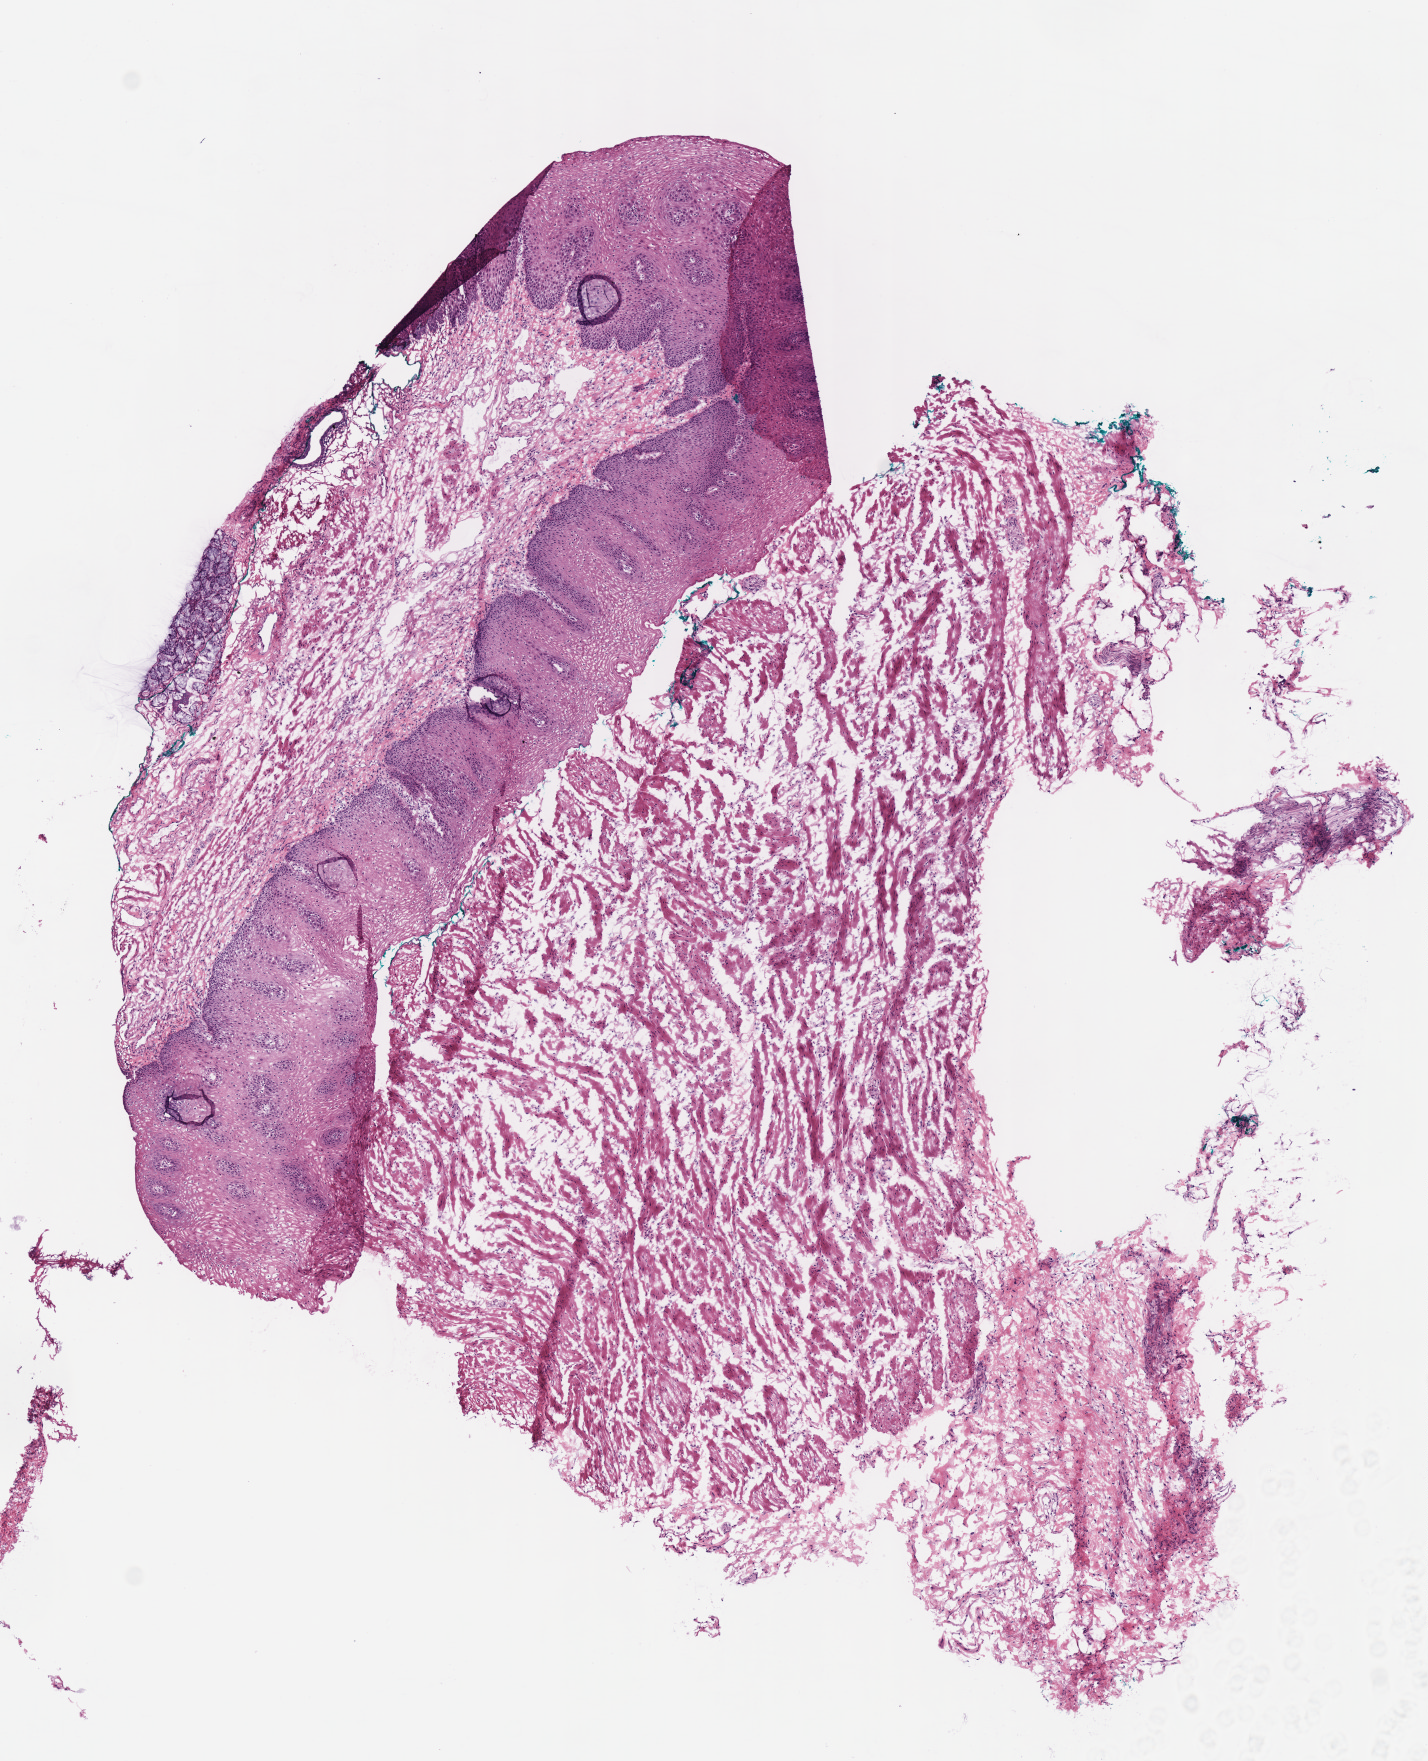
Digitized Hematoxylin and eosin (H&E) stained tissue section (whole slide) — low-resolution overview of the scanned area, about 5.6 x 6.9 mm (acquisition: 40x scan); frozen section from the top of the tissue portion; stomach, solid tissue normal (non-tumour tissue) sample. Male patient; age at initial diagnosis 69 years.
- this section: solid tissue normal (non-tumour) sample from the same patient
- patient diagnosis: Mucinous adenocarcinoma (cardia, NOS)